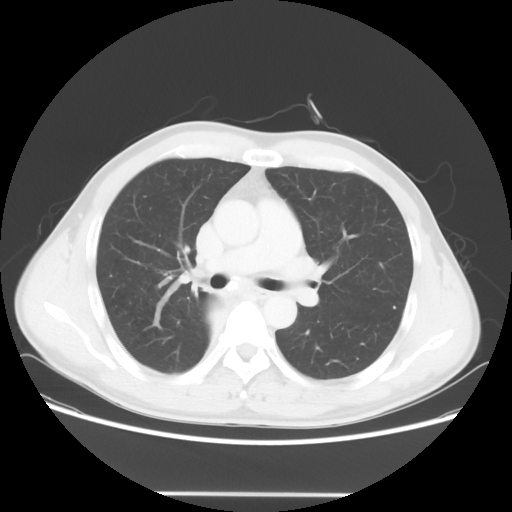
Chest CT, one axial slice; reconstruction kernel STANDARD; 120 kVp; lung window (W 1500 / L -600 HU); 5 mm slice thickness; 512 × 512 image matrix. Male patient, age 47 years. From the clinical record (not read from this slice): clinical TNM (as recorded): T2 N0 M0; histopathological grade: G2.
Annotated regions visible in this slice (rectangle marked by the reading radiologist):
- lung tumour (recorded histology: squamous cell carcinoma): bounding box (x1, y1, x2, y2) in pixels: (197, 295, 232, 335)